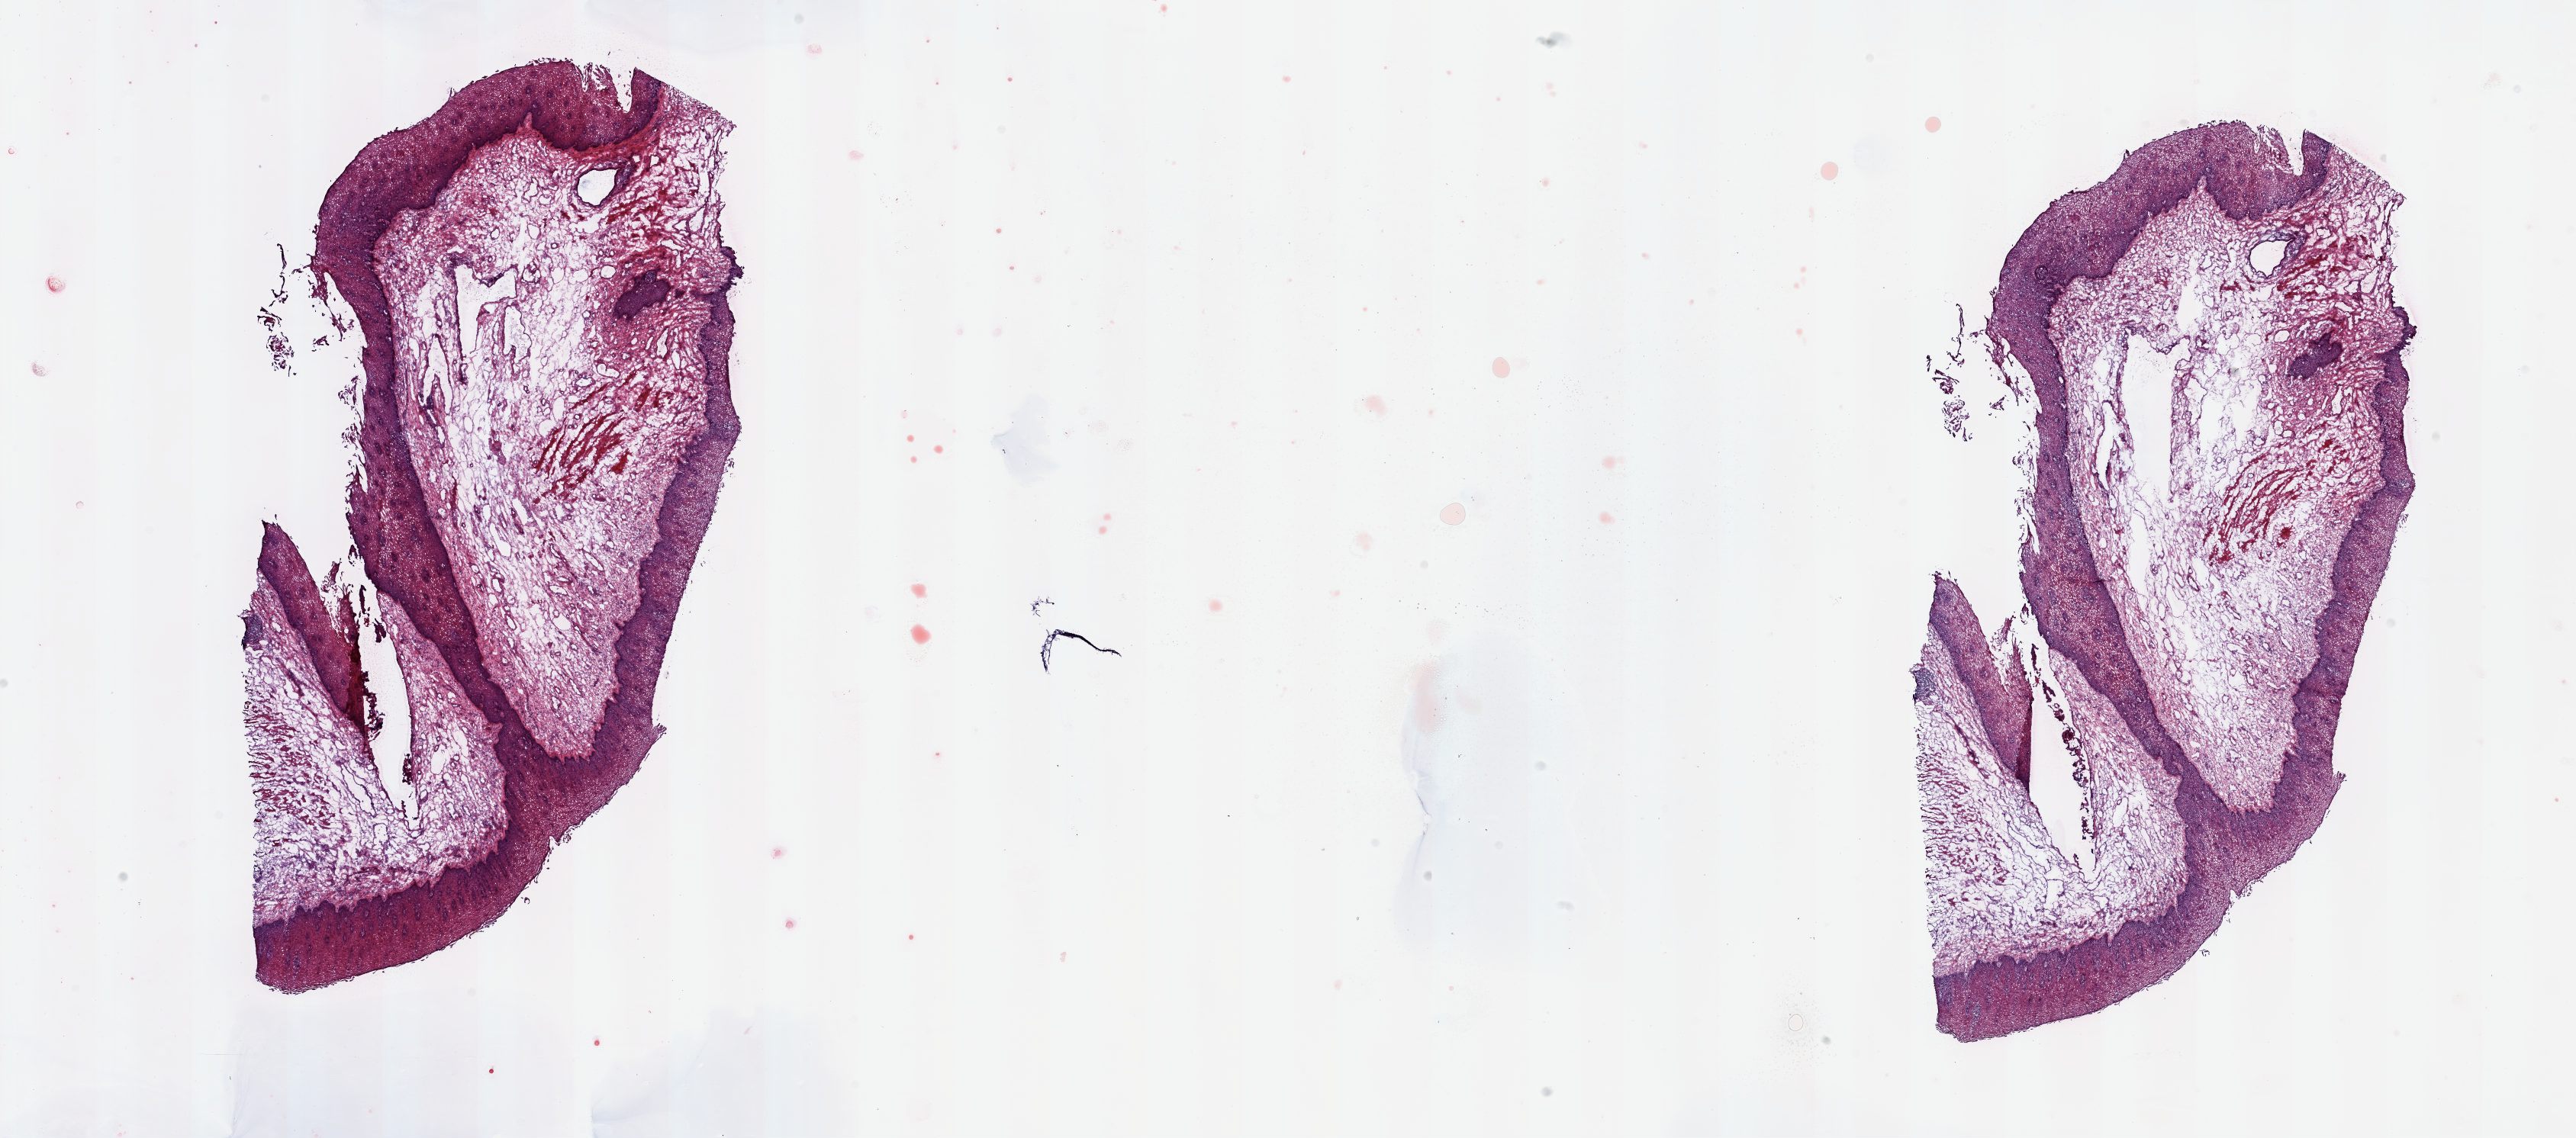
Whole-slide histology image, Hematoxylin and eosin (H&E) stained, a low-resolution overview of the entire scanned area, about 26.8 x 11.8 mm (slide scanned at 20x), frozen section, solid tissue normal (non-tumour tissue) sample from the stomach. Male patient; age at initial diagnosis 63 years. Composition of this section per pathologist review: tumour cells 0%, tumour nuclei 0%, normal cells 100%, stromal cells 0%, necrosis 0%. Inflammatory infiltration, as recorded: lymphocyte infiltration 3%, monocyte infiltration 0%, neutrophil infiltration 0%.
• this section: solid tissue normal (non-tumour) sample from the same patient
• patient diagnosis: Adenocarcinoma, NOS (cardia, NOS)